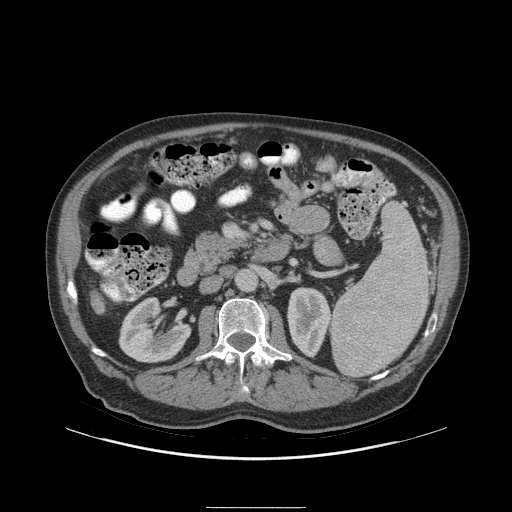
Contrast-enhanced abdominal CT (liver protocol), one axial slice. Position 26 of 105 along the scan axis. Reconstruction kernel STANDARD. Soft-tissue window (W 400 / L 40 HU). 2.5 mm slice thickness. 512 × 512 image matrix, field of view 440 × 440 mm. Case-level facts recorded for this patient, not image findings: diagnosis: hepatocellular carcinoma (patient treated with transarterial chemoembolisation; whether this scan precedes or follows treatment is not stated here); TNM stage (as recorded): Stage-I; Child-Pugh class: A; tumour nodularity: uninodular.
Structures marked on this image (semi-automatically segmented with operator editing):
- liver parenchyma outside the tumour (the mass and vessels are separate outlines, so this box may not span the whole liver): box from (x=90, y=292) to (x=104, y=313) px